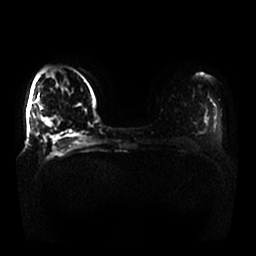
Breast MRI, one axial slice; slice 8 of 25 in the series (ordered by position); diffusion-weighted series; image 2 of 4 stored at this slice position (different b-values; order by instance number); 1.5 T; 4 mm slice thickness; 256 × 256 image matrix, field of view 370 × 370 mm. Female patient.
Outlined on this slice (outlined manually by an expert reader):
- tumour on diffusion-weighted imaging: bounding box <45,119,52,126> (left, top, right, bottom; pixels)